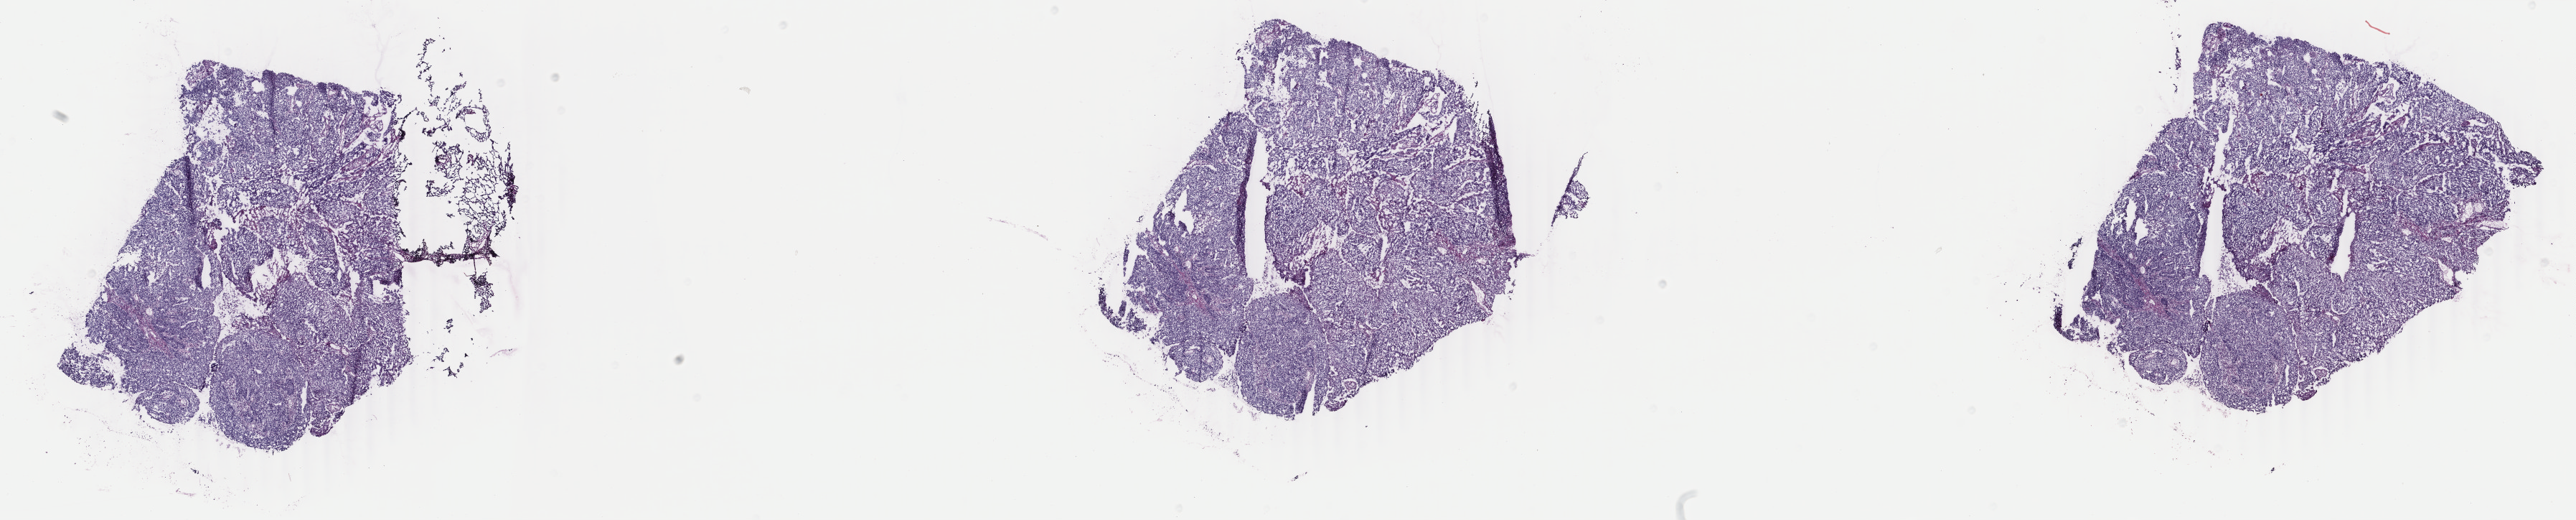
Whole-slide histology image, H&E — shown as a low-resolution overview of the whole scanned area (about 28.6 x 5.8 mm). Frozen section from the bottom of the tissue portion. Uterus, primary tumour sample. Patient: female, age at initial diagnosis 65 years. Histologic grade: G3 (poorly differentiated). Composition of this section per pathologist review: tumour cells 100%, tumour nuclei 90%, normal cells 0%, stromal cells 0%, necrosis 0%. Inflammatory infiltration, as recorded: lymphocyte infiltration 0%, monocyte infiltration 0%, neutrophil infiltration 0%.
- diagnosis: Endometrioid adenocarcinoma, NOS (endometrium)
- FIGO stage: IB